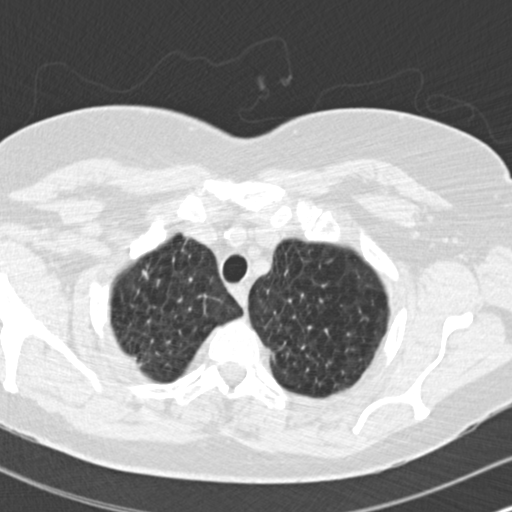
Low-dose screening chest CT, axial slice; baseline annual screen; lung window (W 1500 / L -600 HU); 512 × 512 image matrix, field of view 310 × 310 mm. Female, age 73 years at enrolment. Former smoker at enrolment.
• Expert reader's lesion annotation, bounding box (x1, y1, x2, y2) in pixels: (126, 252, 169, 291).
• The screening reader recorded 2 non-calcified nodules or masses ≥4 mm on this exam (right upper lobe, right upper lobe); which of them this box marks is not recorded.
• Official screen result: positive, change unspecified: nodule(s) >= 4 mm or enlarging nodule(s), mass(es), or other non-specific abnormalities suspicious for lung cancer.
• Participant outcome: lung cancer diagnosed 601 days after this screen (after the second annual screen) — adenocarcinoma, NOS, right upper lobe, moderately differentiated (G2), stage IB (AJCC 6th edition), 15 mm at pathology.